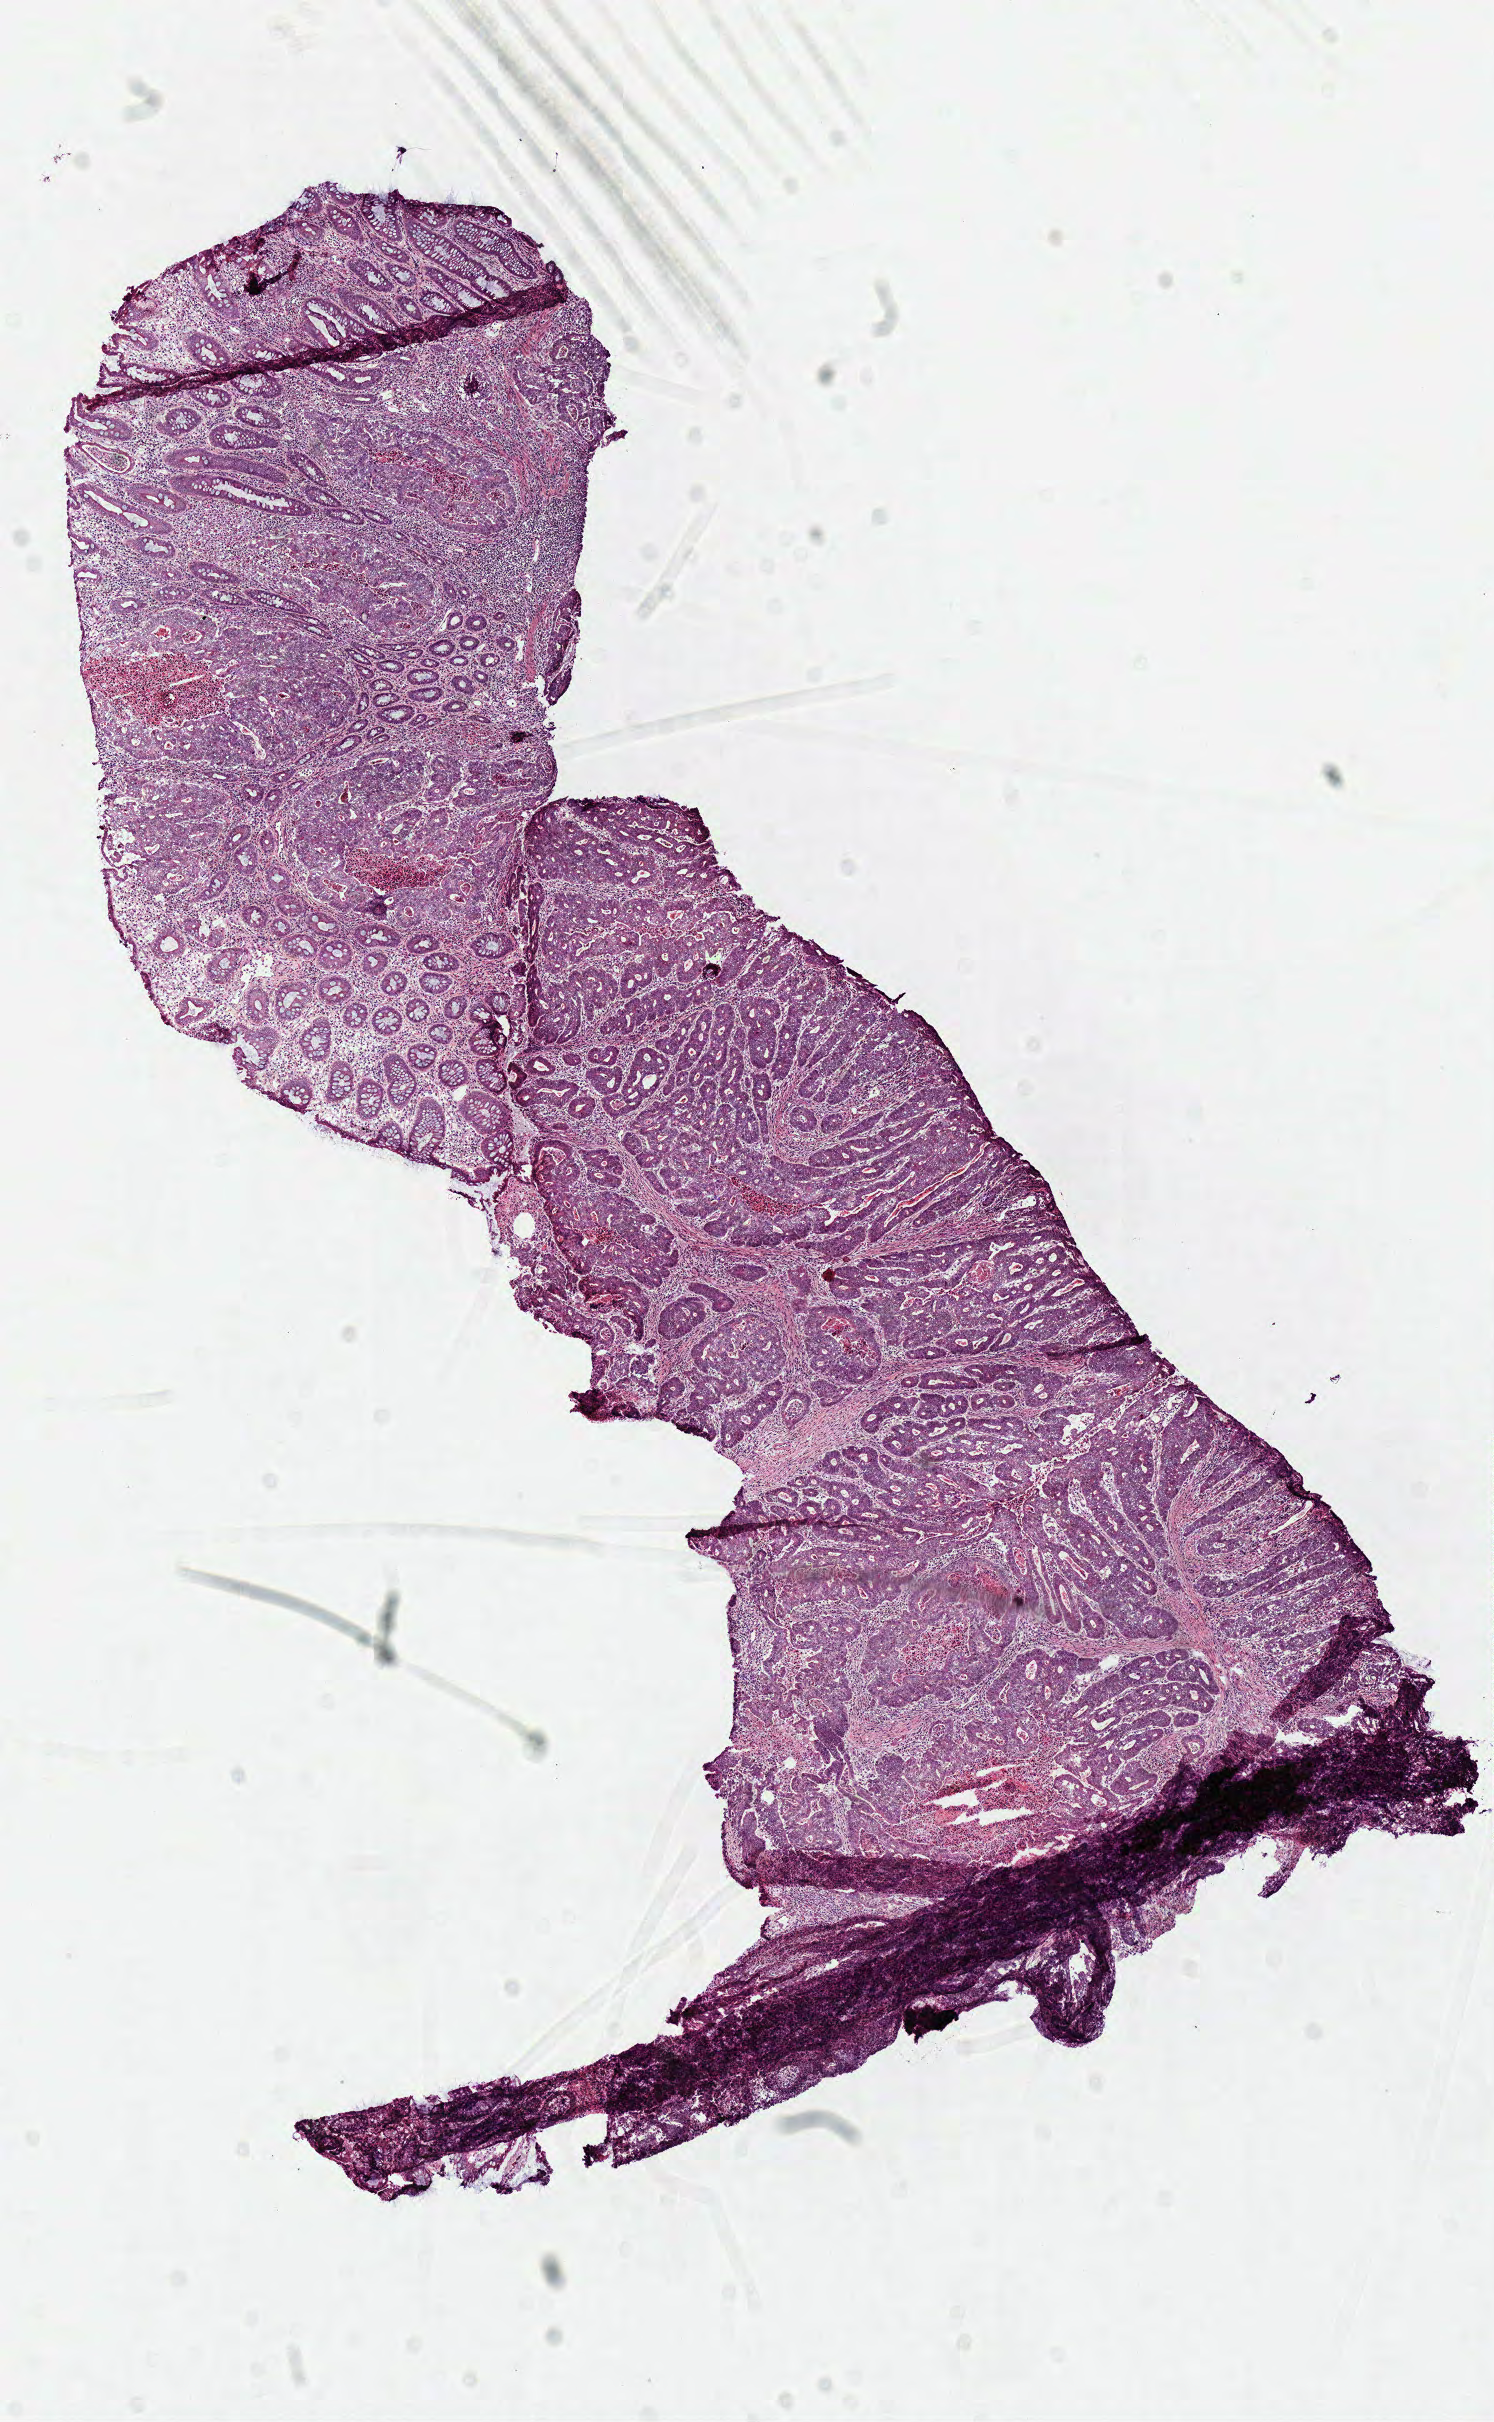
Whole-slide histology image, H&E-stained — low-resolution overview of the scanned area, about 5.9 x 9.5 mm (slide scanned at 40x); frozen section from the top of the tissue portion; sample: primary tumour, colon. Male patient; age at initial diagnosis 71 years. Composition of this section per pathologist review: tumour cells 67%, tumour nuclei 80%, normal cells 10%, stromal cells 15%, necrosis 8%.
Diagnosis: Adenocarcinoma, NOS (ascending colon).